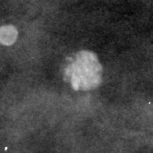
Crop from a digitized film mammogram around one marked abnormality, right breast, MLO view.
Marked abnormality: calcifications, morphology round and regular / eggshell; BI-RADS assessment category 2; benign without callback (not worked up further).